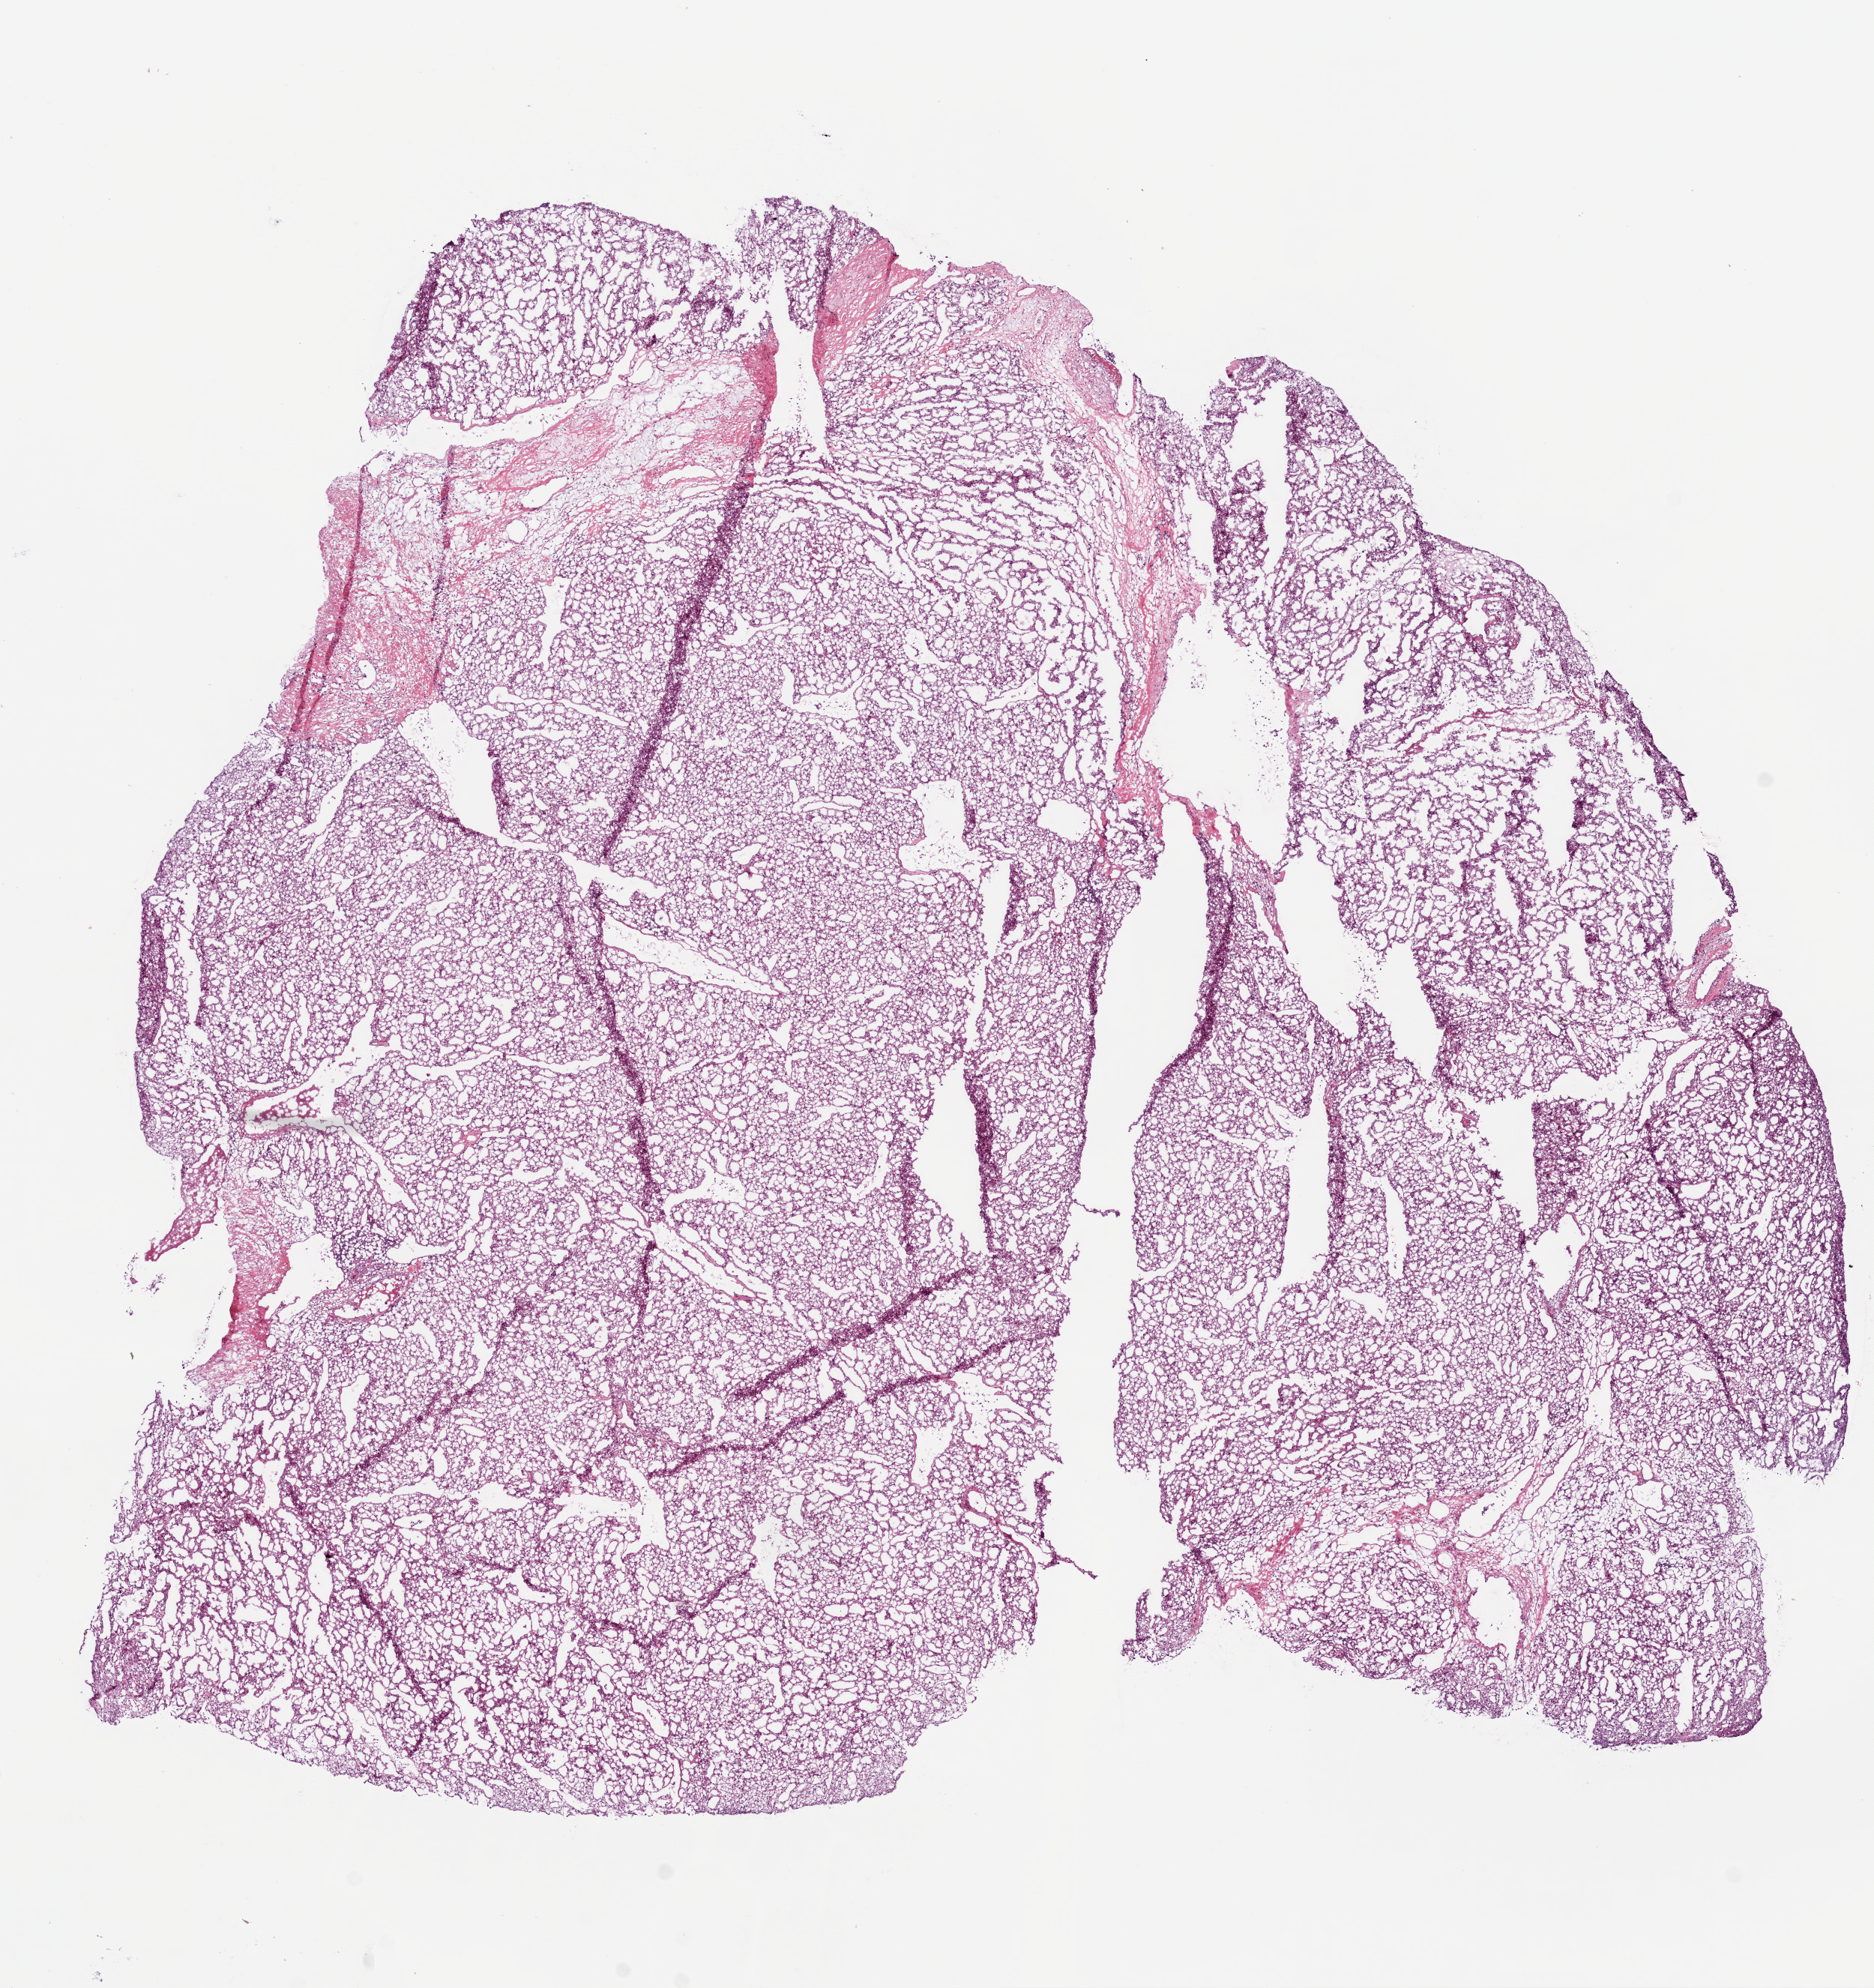
Whole-slide histology image, H&E-stained — shown as a low-resolution overview of the whole scanned area (about 10.0 x 10.6 mm); frozen section from the bottom of the tissue portion; primary tumour sample from the kidney. Male, age 40 years at initial diagnosis. Histologic grade: G3 (poorly differentiated). Pathologist review of this section (percent, as recorded): tumour cells 90%, tumour nuclei 85%, normal cells 0%, stromal cells 10%, necrosis 0%.
Diagnosis: Clear cell adenocarcinoma, NOS. AJCC pathologic stage: I.